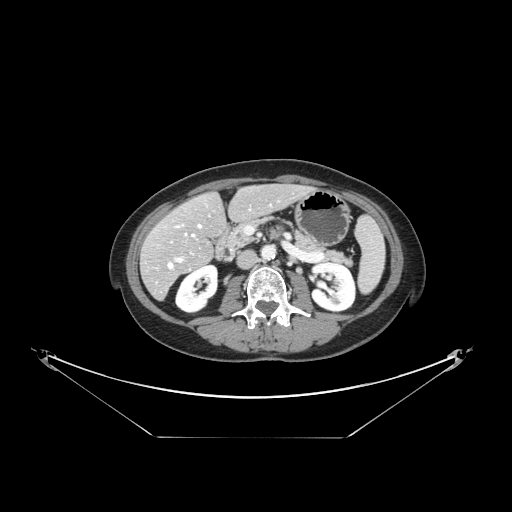
Contrast-enhanced abdominal CT, one axial slice; slice 59 of 148 in the series (ordered by position); 120 kVp; intravenous contrast given; soft-tissue window (W 400 / L 40 HU); 2.5 mm slice thickness; 512 × 512 image matrix, field of view 500 × 500 mm. Female patient, age 73 years. From the clinical record (not read from this slice): diagnosis: colorectal cancer liver metastases, imaged before liver resection; multiple liver metastases: no; largest metastasis: 1 cm; chemotherapy before resection: yes.
Outlined on this slice (expert manual segmentation):
- hepatic veins: bounding box [x1, y1, x2, y2] px = [168, 224, 201, 268]
- liver: [142, 185, 309, 298]
- planned liver remnant (the part of the liver to remain after resection): [165, 185, 307, 249]
- portal vein (with intrahepatic branches): [175, 258, 182, 262]